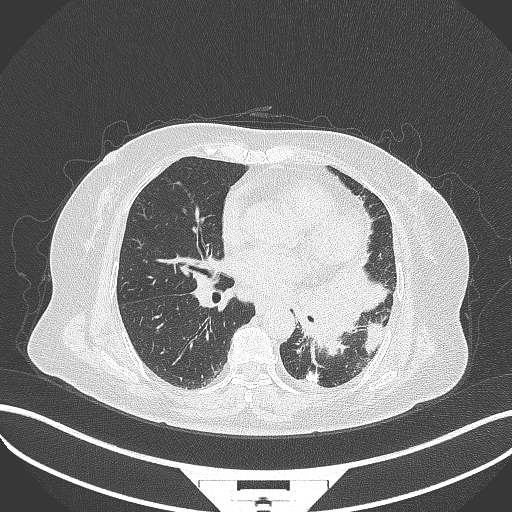
Chest CT, one axial slice; position 166 of 322 along the scan axis; reconstruction kernel B70f; 120 kVp; lung window (W 1500 / L -600 HU); 512 × 512 image matrix, field of view 400 × 400 mm. Patient: female, 69 years. Case-level facts recorded for this patient, not image findings: clinical TNM (as recorded): T2b N3 M1.
Annotated regions visible in this slice (rectangle marked by the reading radiologist):
- lung tumour (recorded histology: adenocarcinoma): box from (x=295, y=254) to (x=390, y=358) px